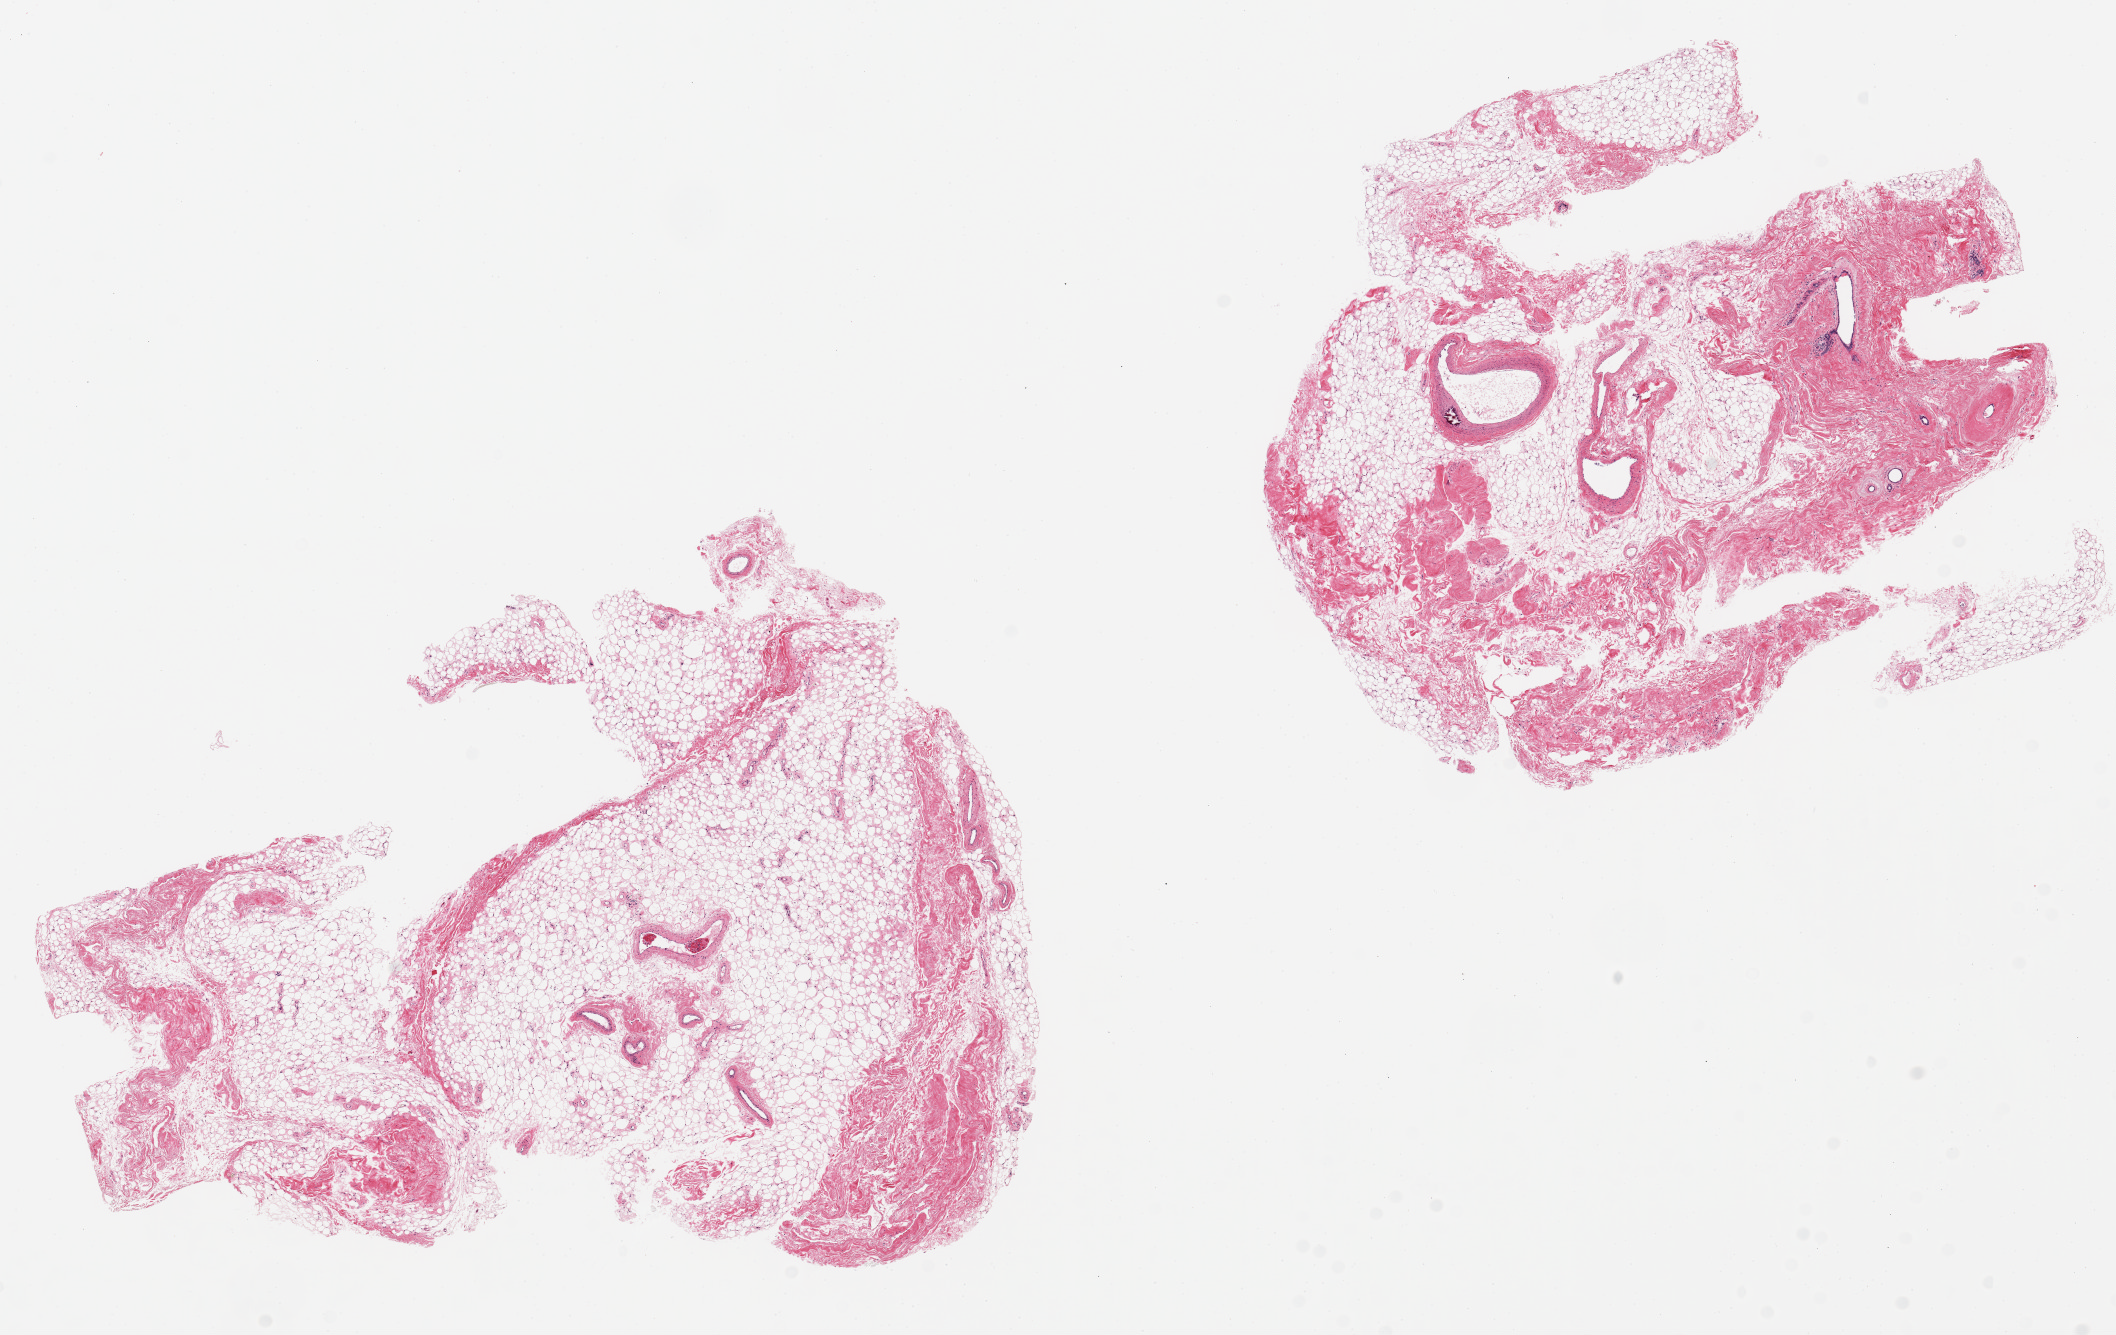
Digitized H&E-stained section, shown as a low-resolution overview of the whole scanned area (about 16.7 x 10.6 mm), PAXgene-fixed paraffin-embedded (PFPE) section, target tissue: breast, tissue donor sample. Donor: female.
Pathologist's review note for this sample: 2 pieces, 8x6 & 6x6mm; atrophy; a few ducts in 1 piece.